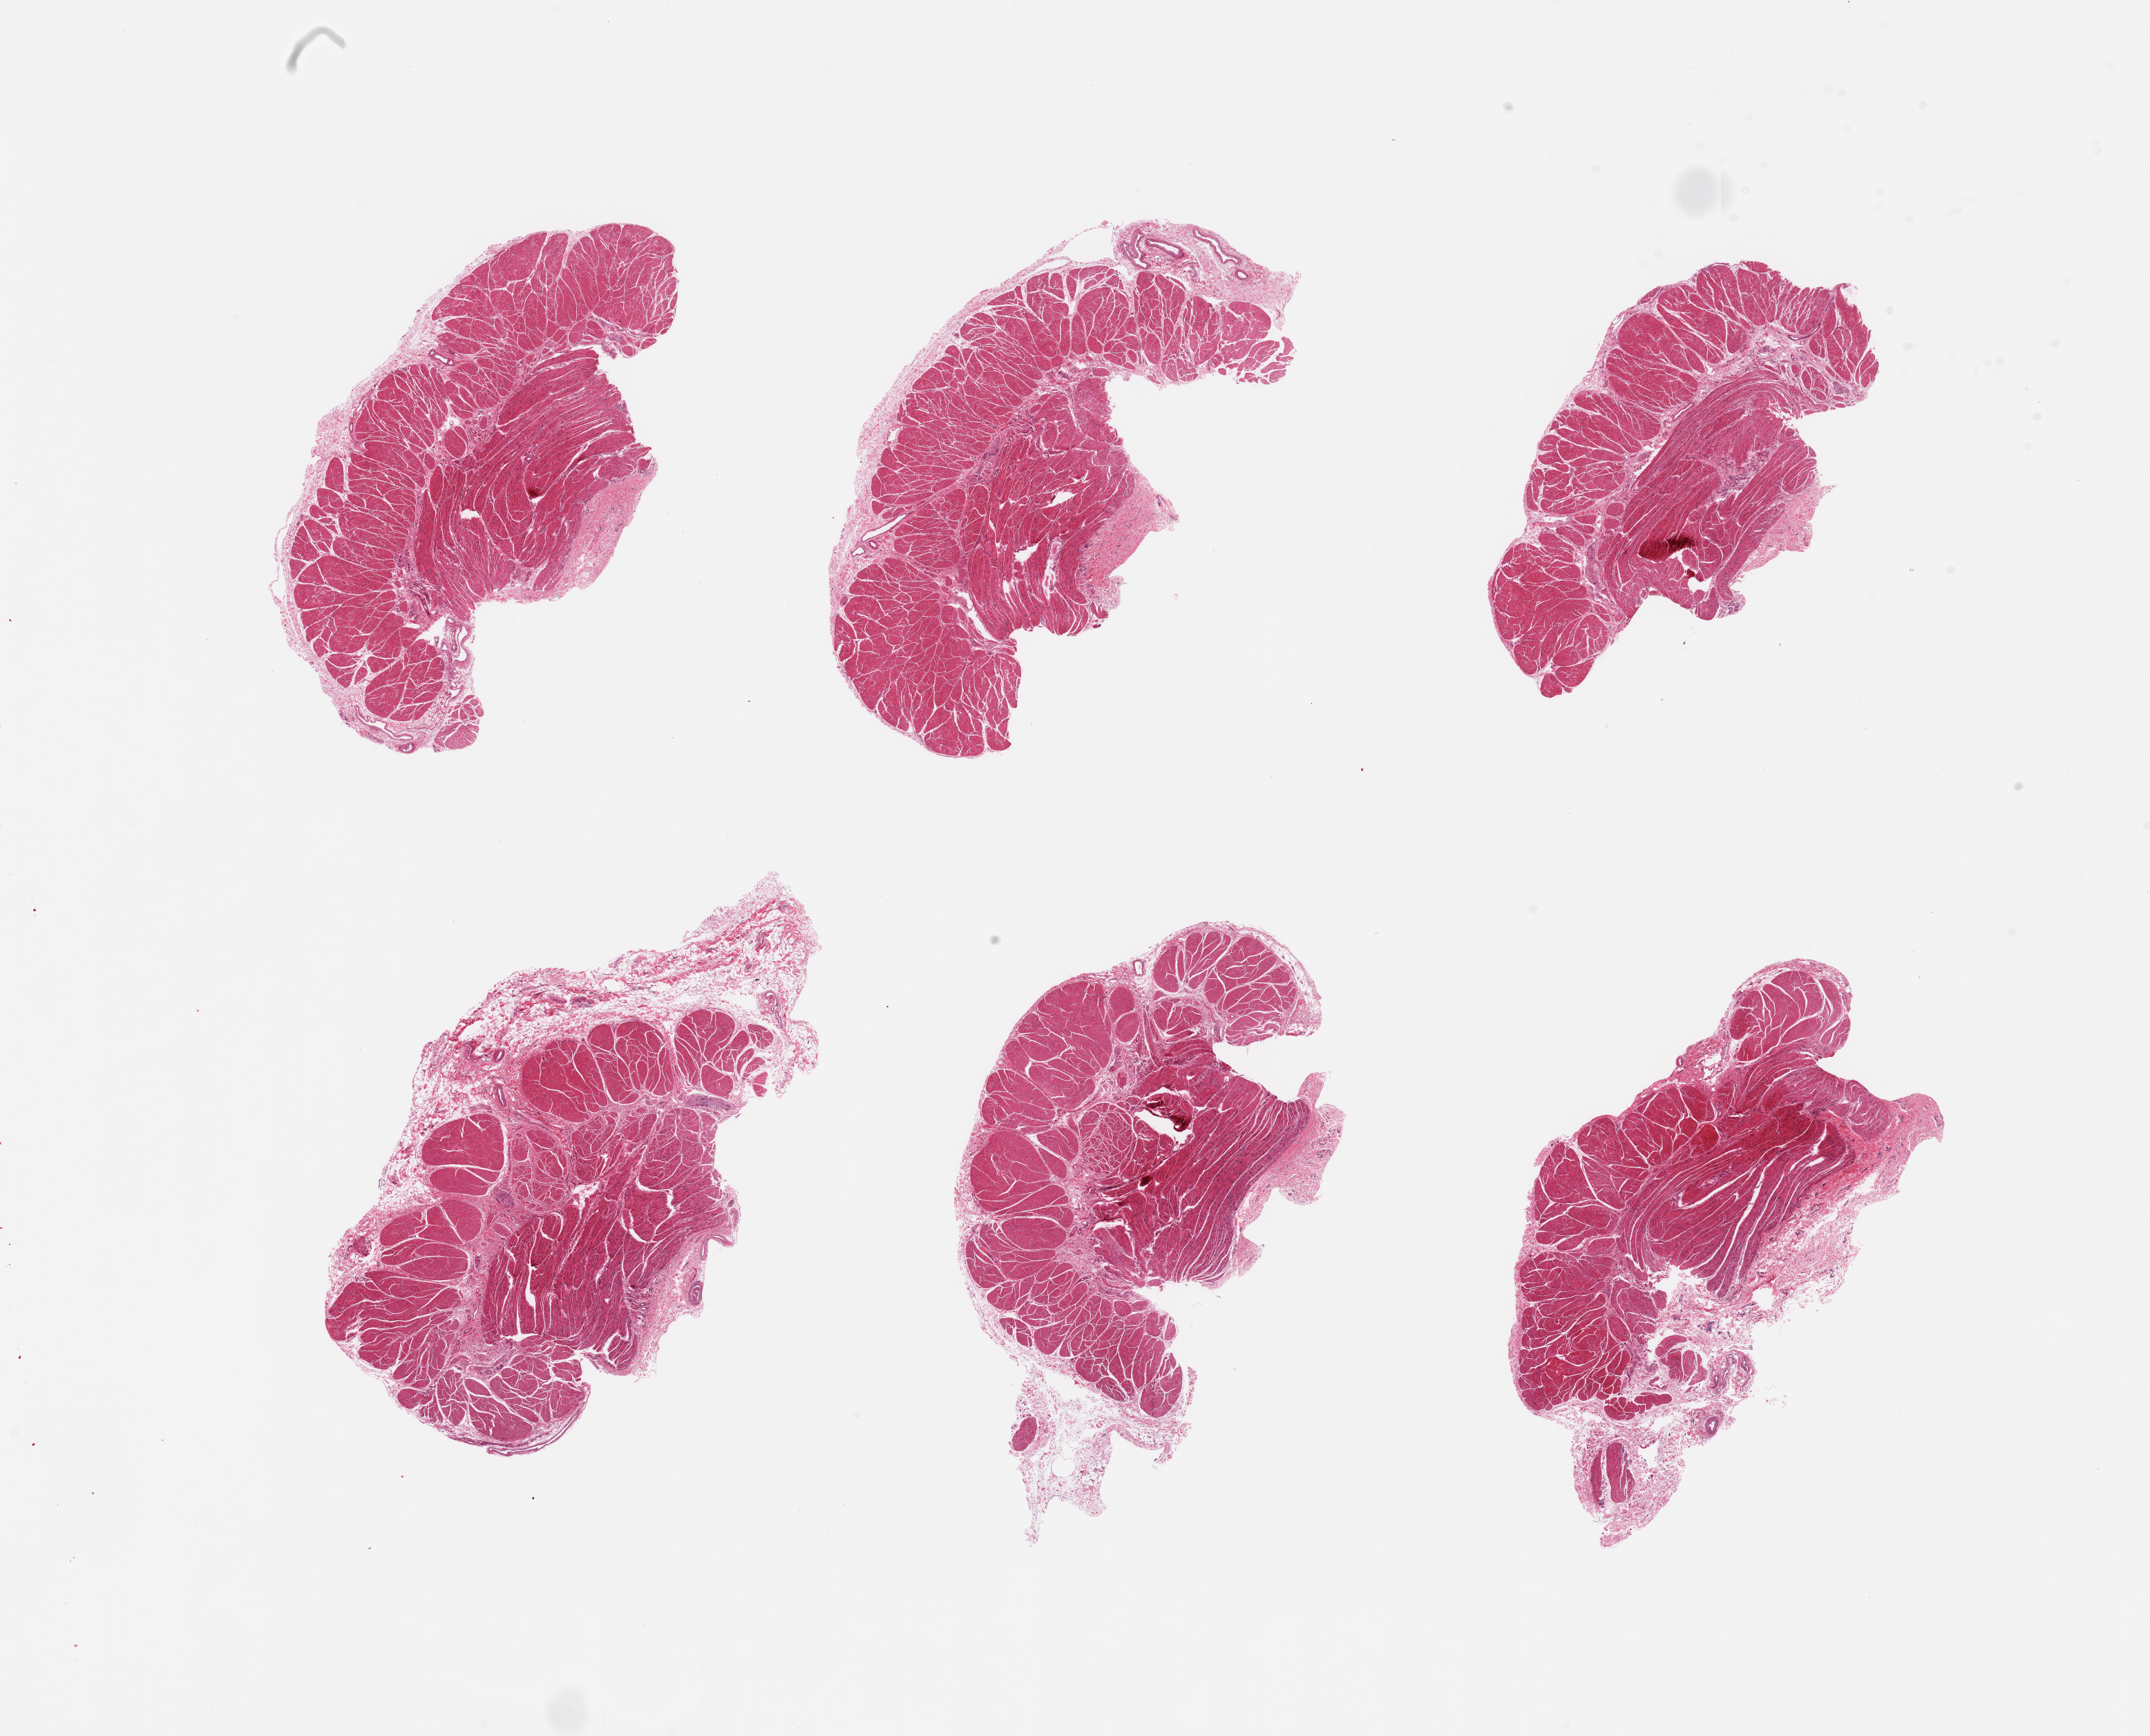
Digitized H&E-stained section, brightfield, a low-resolution overview of the entire scanned area, about 24.6 x 19.9 mm. PAXgene-fixed, paraffin-embedded tissue. Sampled site (target tissue): esophageal muscle. Tissue donor sample.
• review note (as recorded): 6 pieces, confirmed target muscularis